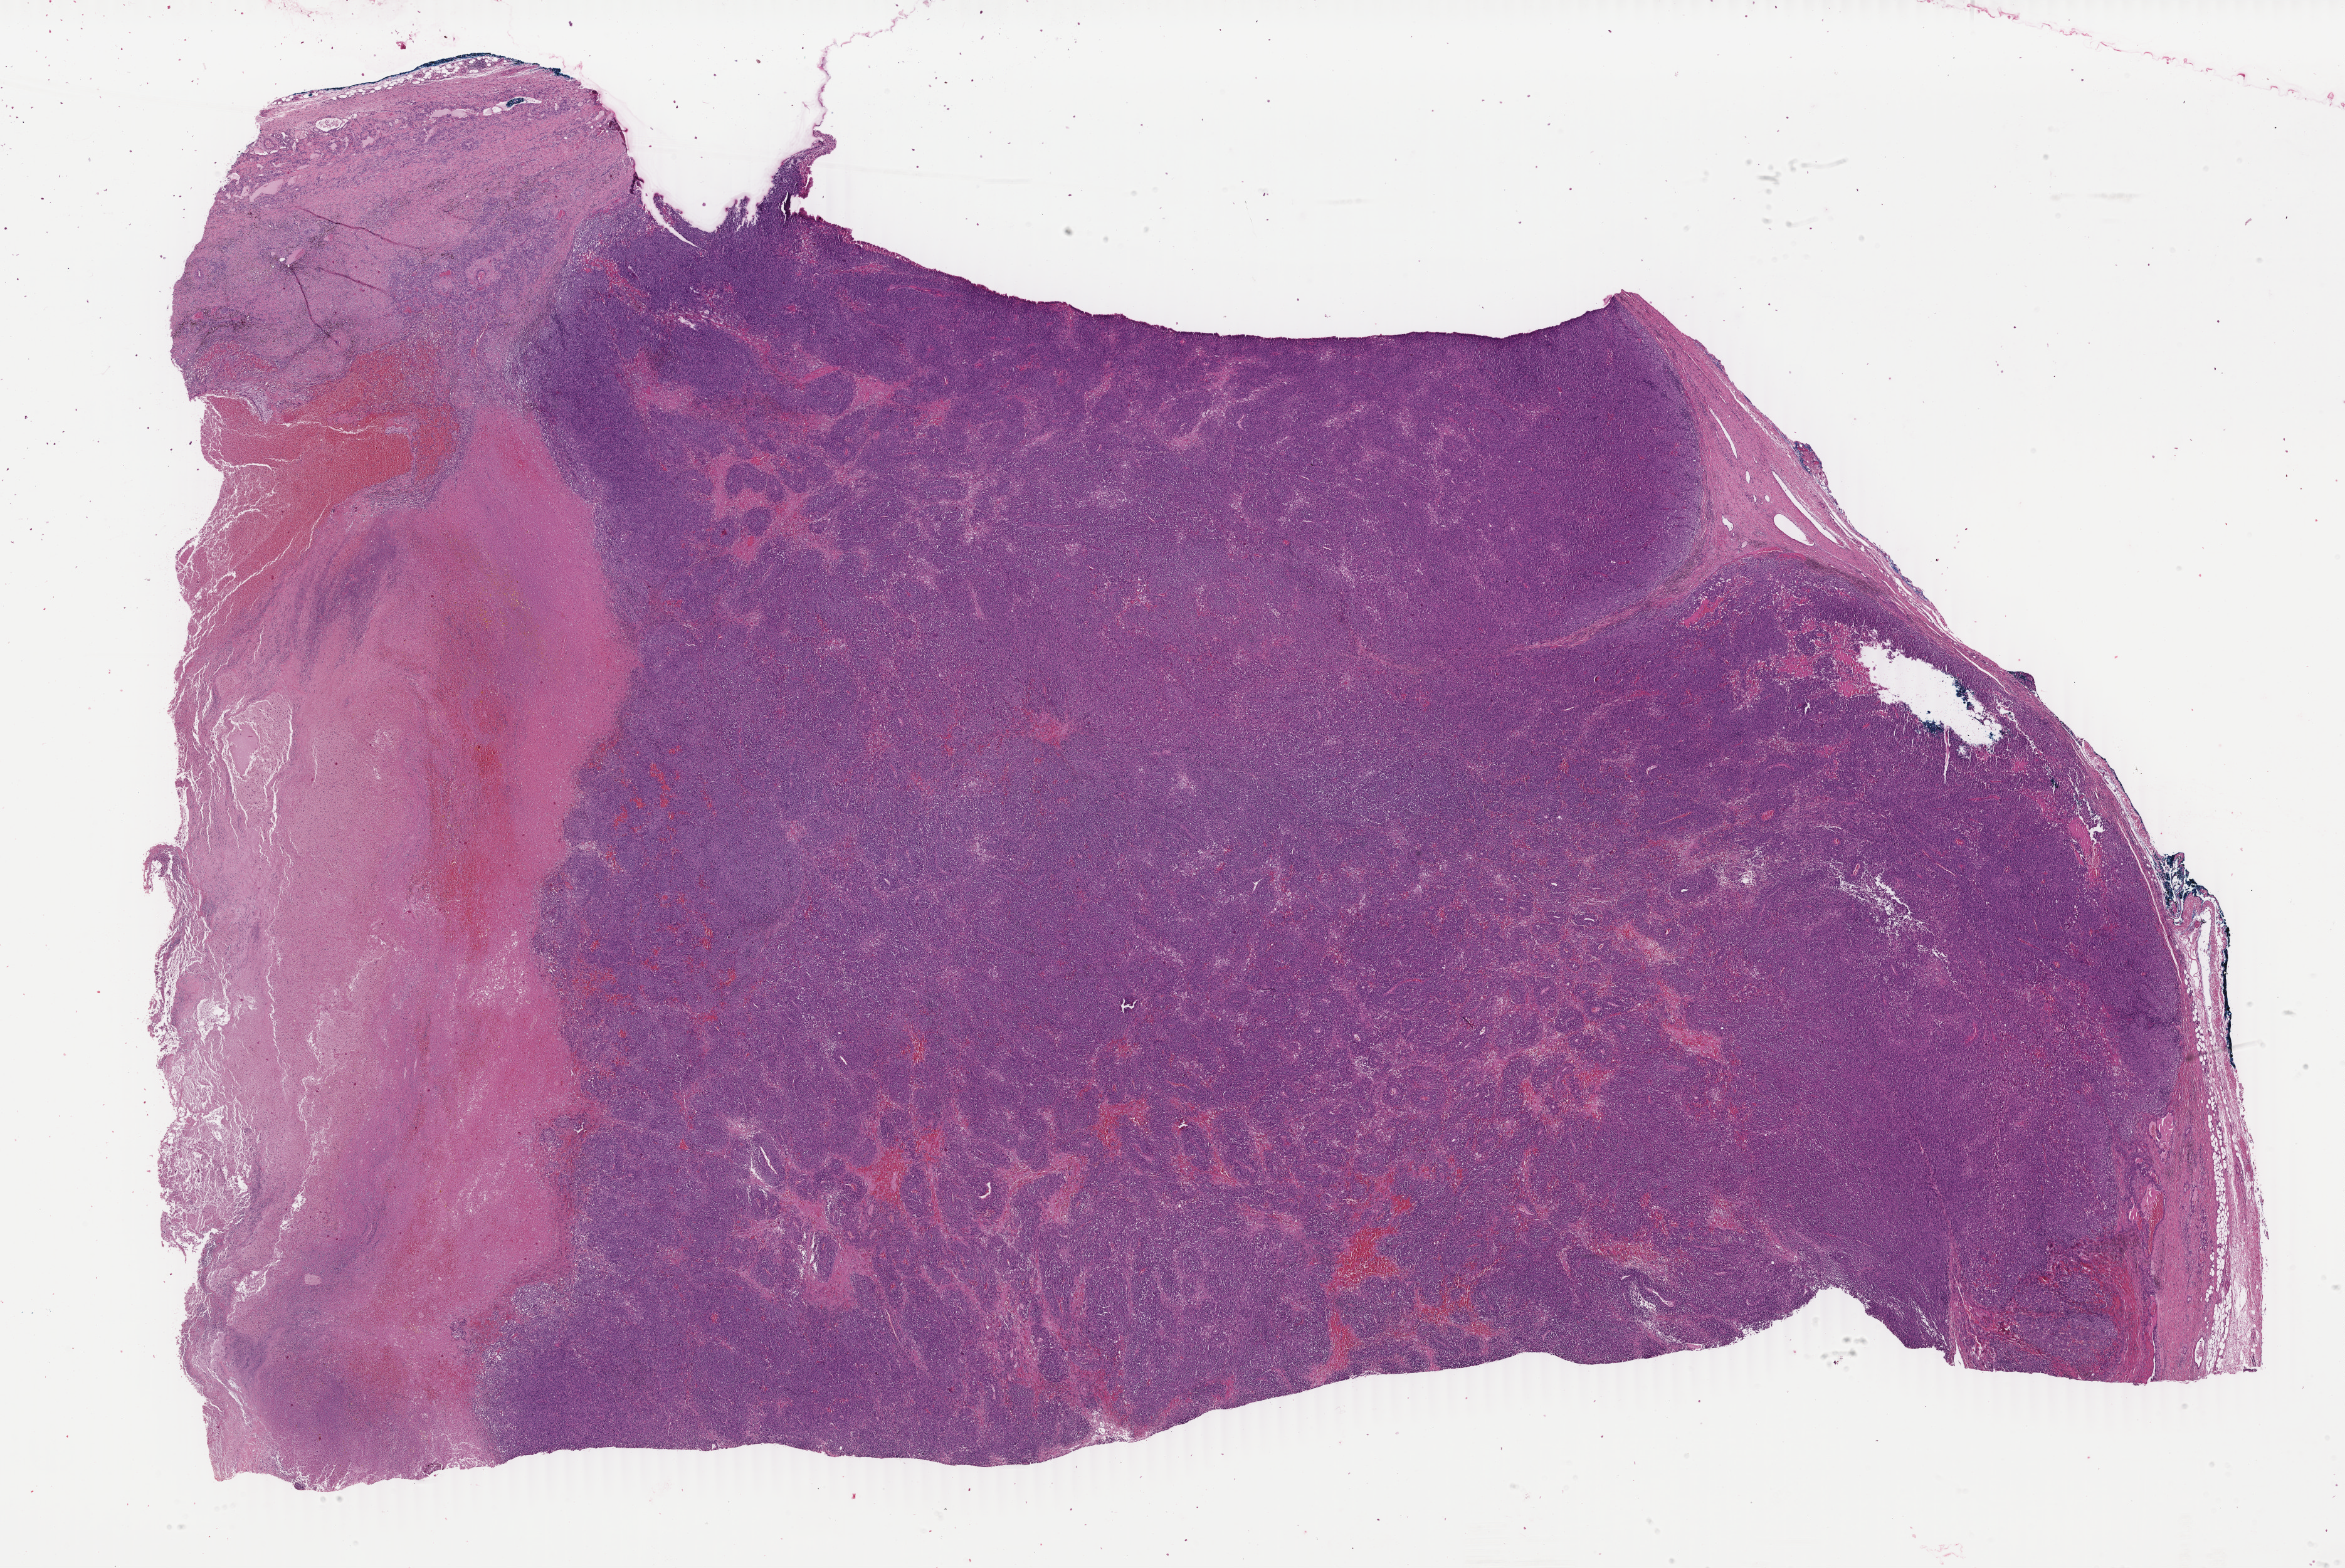
Digitized H&E-stained tissue section (whole slide) — a low-resolution overview of the entire scanned area, about 29.7 x 19.9 mm (slide scanned at 40x). FFPE section. Sample: primary tumour, skin. Female, age 73 years at initial diagnosis.
Diagnosis: Malignant melanoma, NOS.